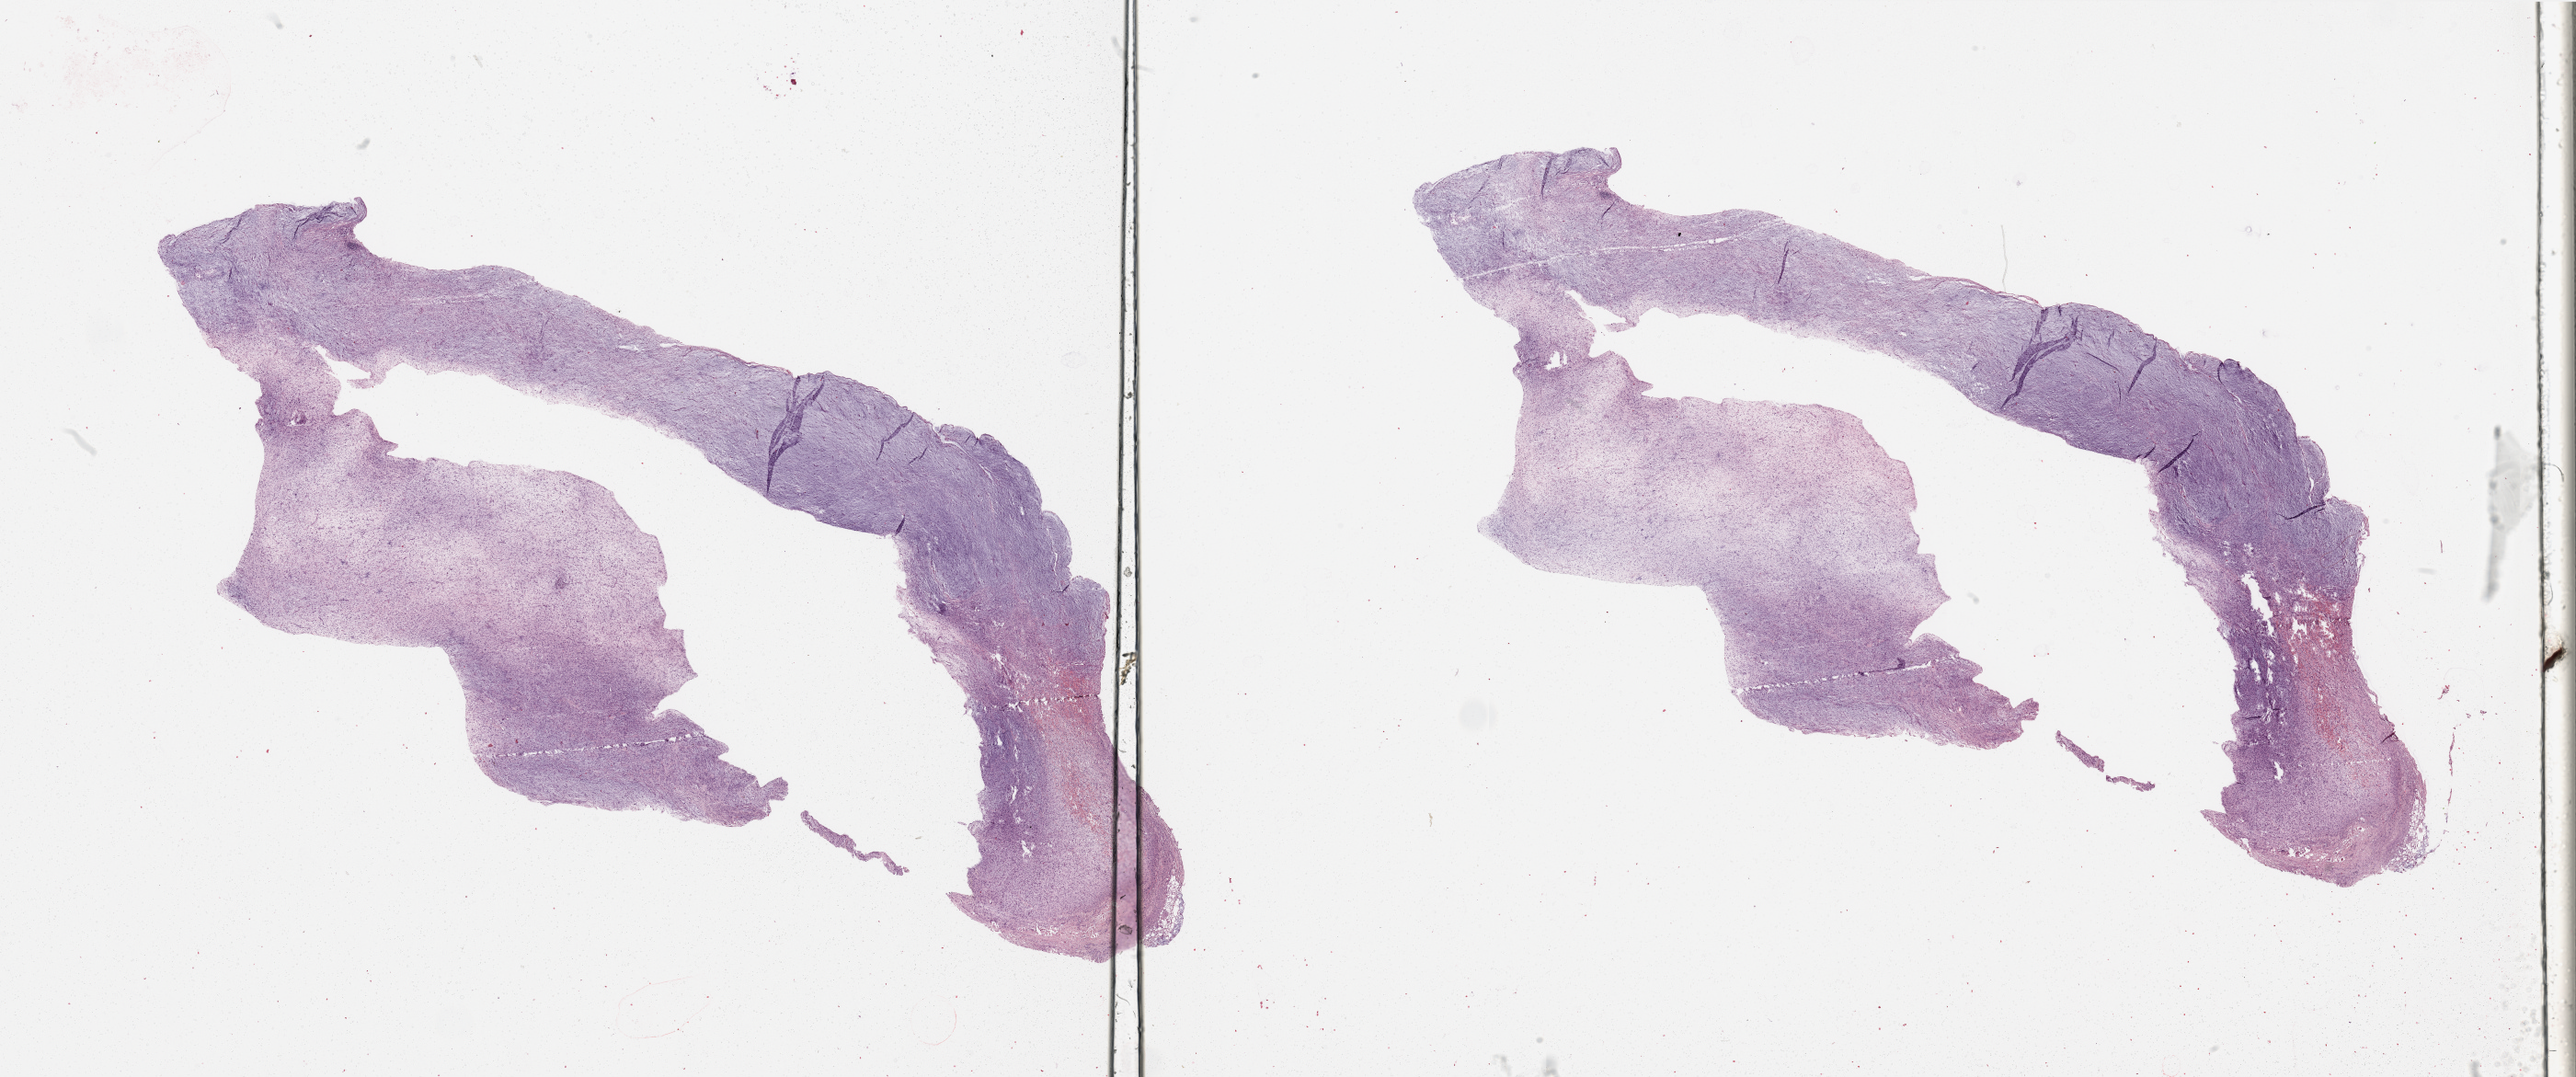
Digitized Hematoxylin and eosin (H&E) stained tissue section (whole slide), whole scanned area (about 44.3 x 18.5 mm, slide scanned at 20x) shown as a low-resolution overview, tumour tissue sample. Patient: male, age 70 years.
- patient diagnosis (cohort enrolment): sarcoma (site not recorded at cohort level)
- primary tumour site (as recorded): lower extremity